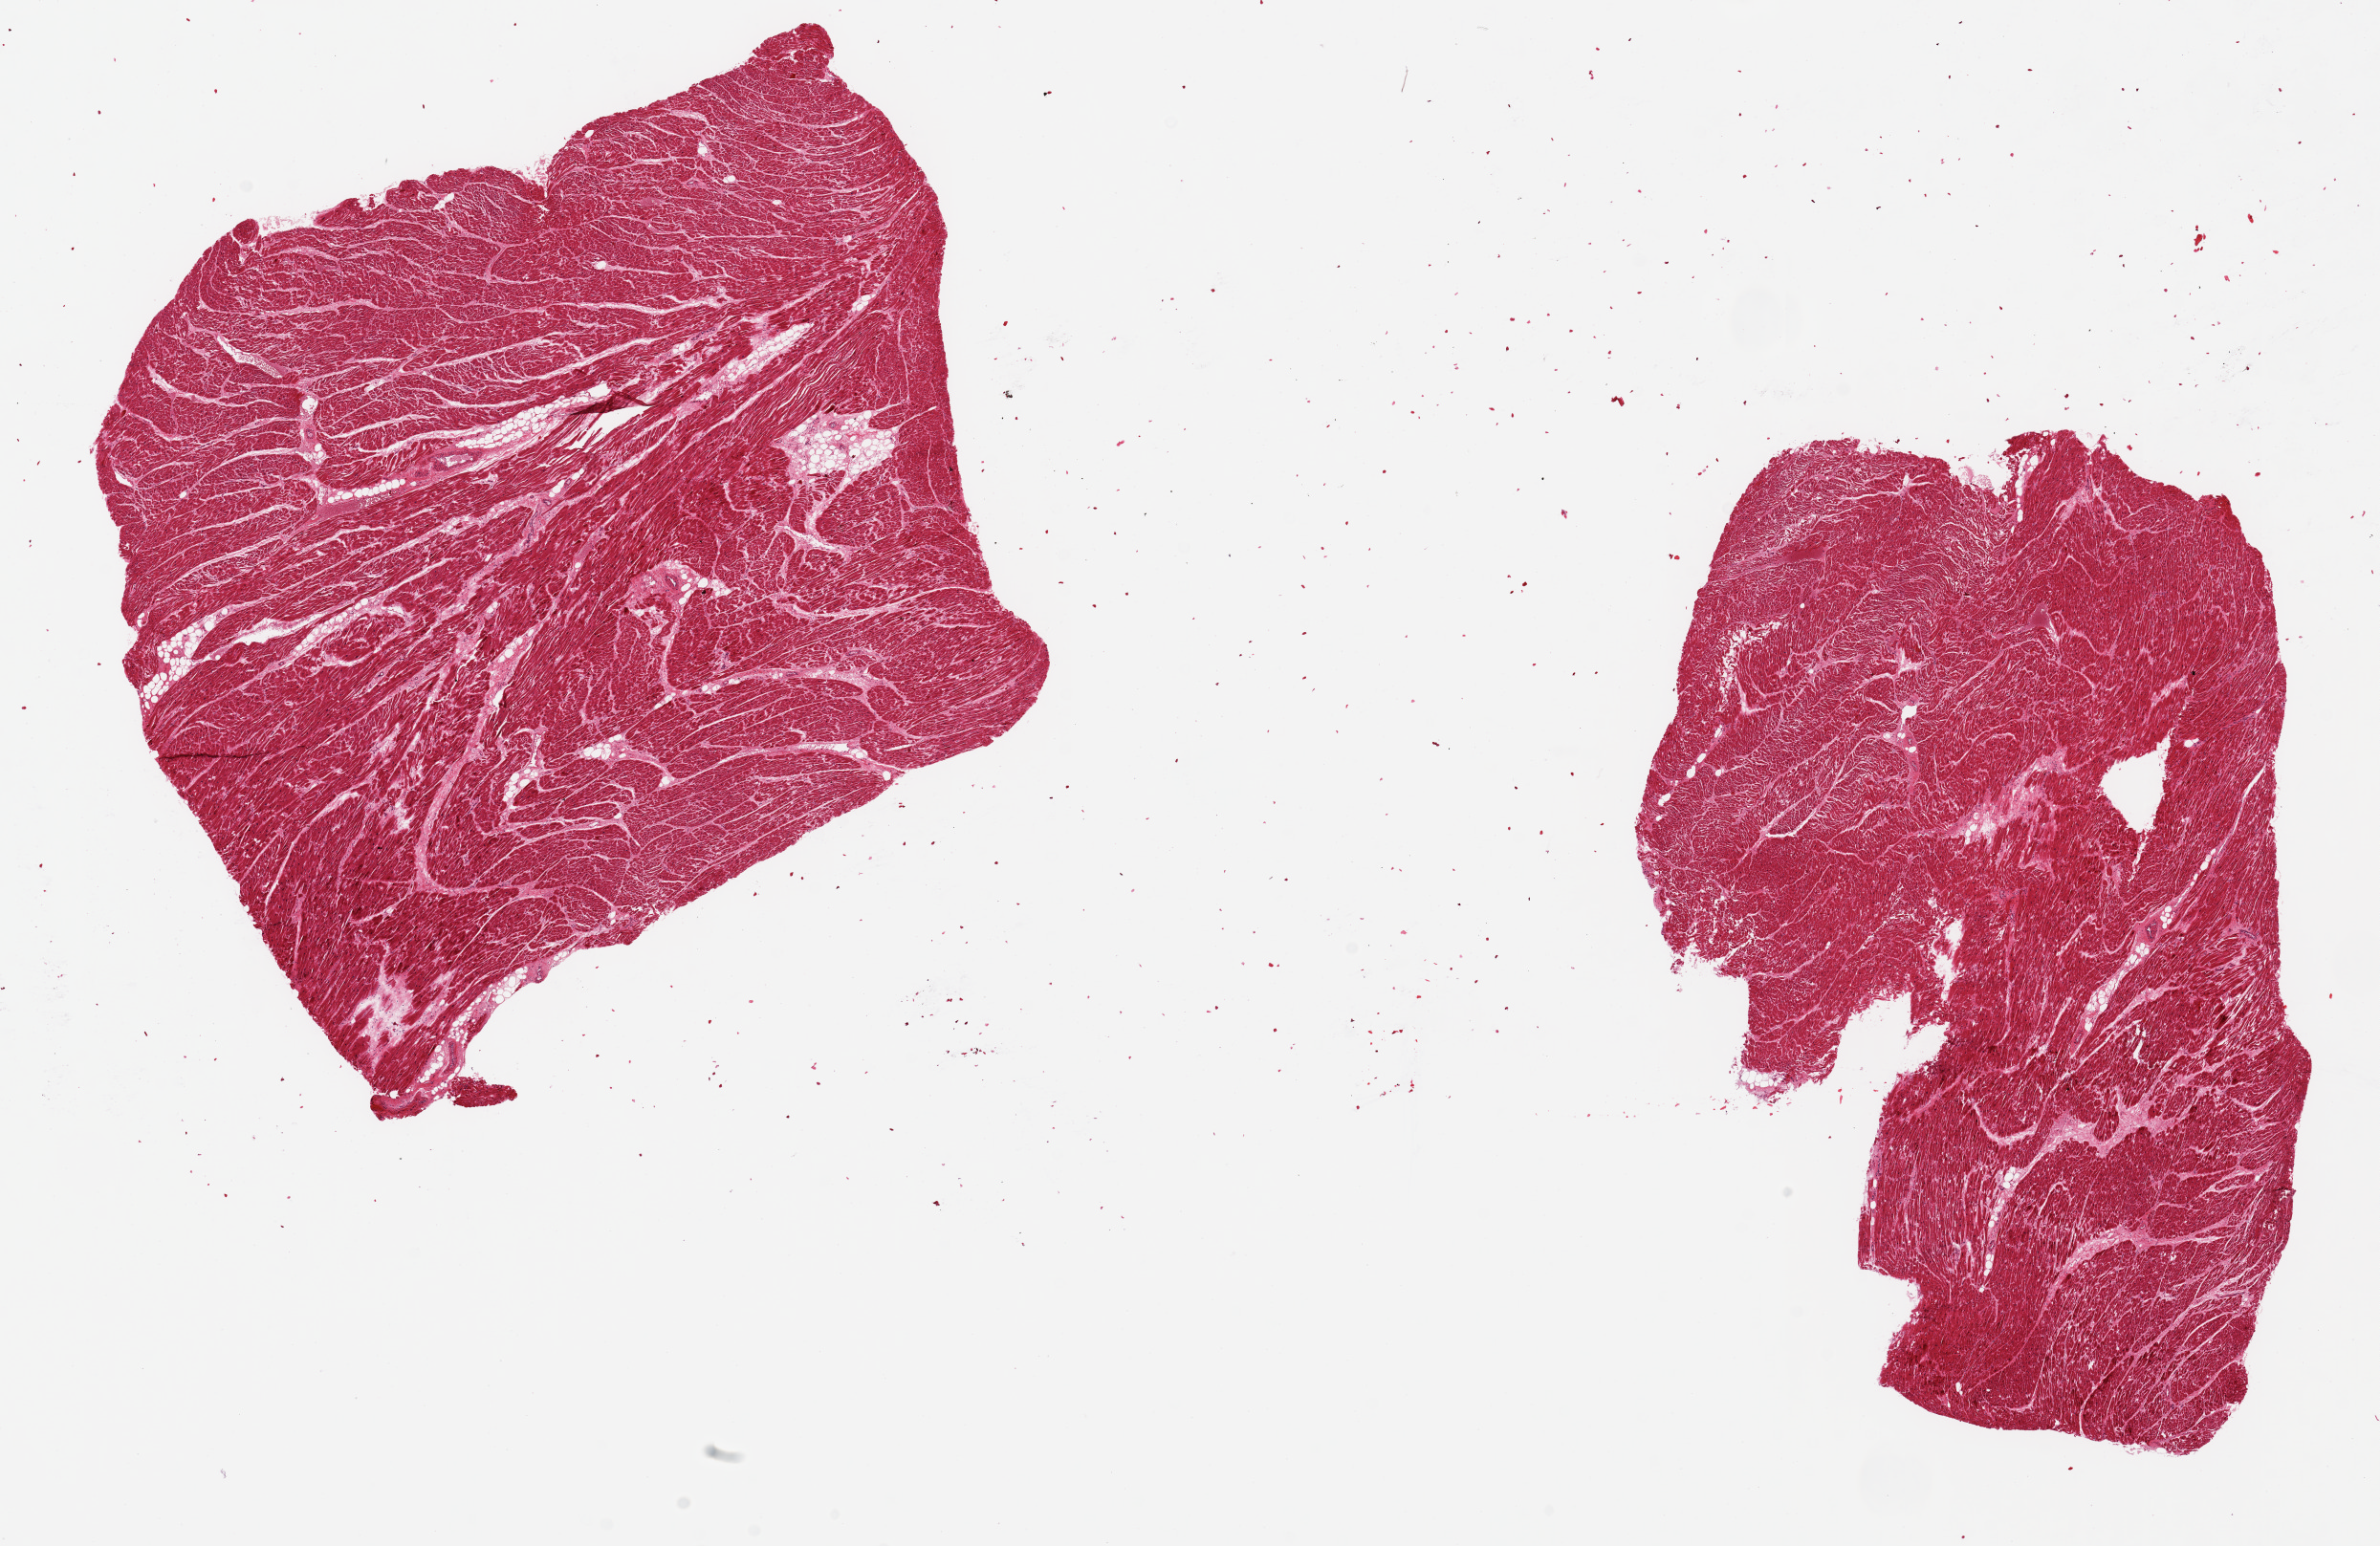
Whole-slide image, H&E stain — a low-resolution overview of the entire scanned area, about 19.7 x 12.8 mm; PAXgene-fixed paraffin-embedded (PFPE) section; sampled site (target tissue): heart; donor tissue sample. Donor sex: male.
Pathologist's review note for this sample: 2 pieces, 8x7mm & 8.5x5.5mm; ~5% internal adipose tissue.